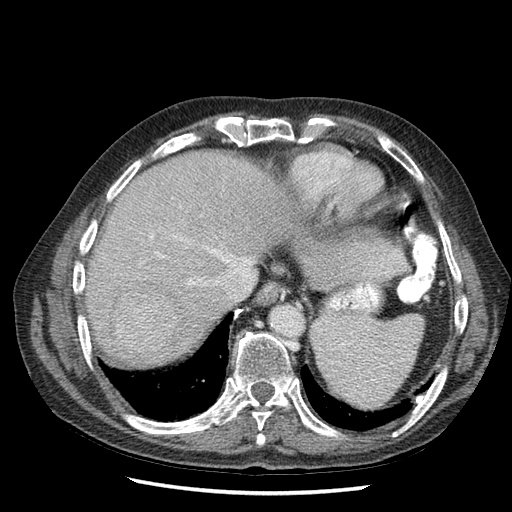
Contrast-enhanced abdominal CT (liver protocol), one axial slice; reconstruction kernel STANDARD; soft-tissue window (W 400 / L 40 HU); 512 × 512 image matrix, field of view 360 × 360 mm. Case-level facts recorded for this patient, not image findings: diagnosis: hepatocellular carcinoma (patient treated with transarterial chemoembolisation; whether this scan precedes or follows treatment is not stated here); TNM stage (as recorded): Stage-I; Child-Pugh class: A; tumour nodularity: uninodular.
Outlined on this slice (semi-automatically segmented with operator editing):
- abdominal aorta: bounding box (x1, y1, x2, y2) in pixels: (271, 305, 302, 334)
- liver parenchyma outside the tumour (the mass and vessels are separate outlines, so this box may not span the whole liver): (81, 150, 308, 368)
- mass: (111, 287, 181, 357)
- liver vessels: (143, 256, 253, 300)